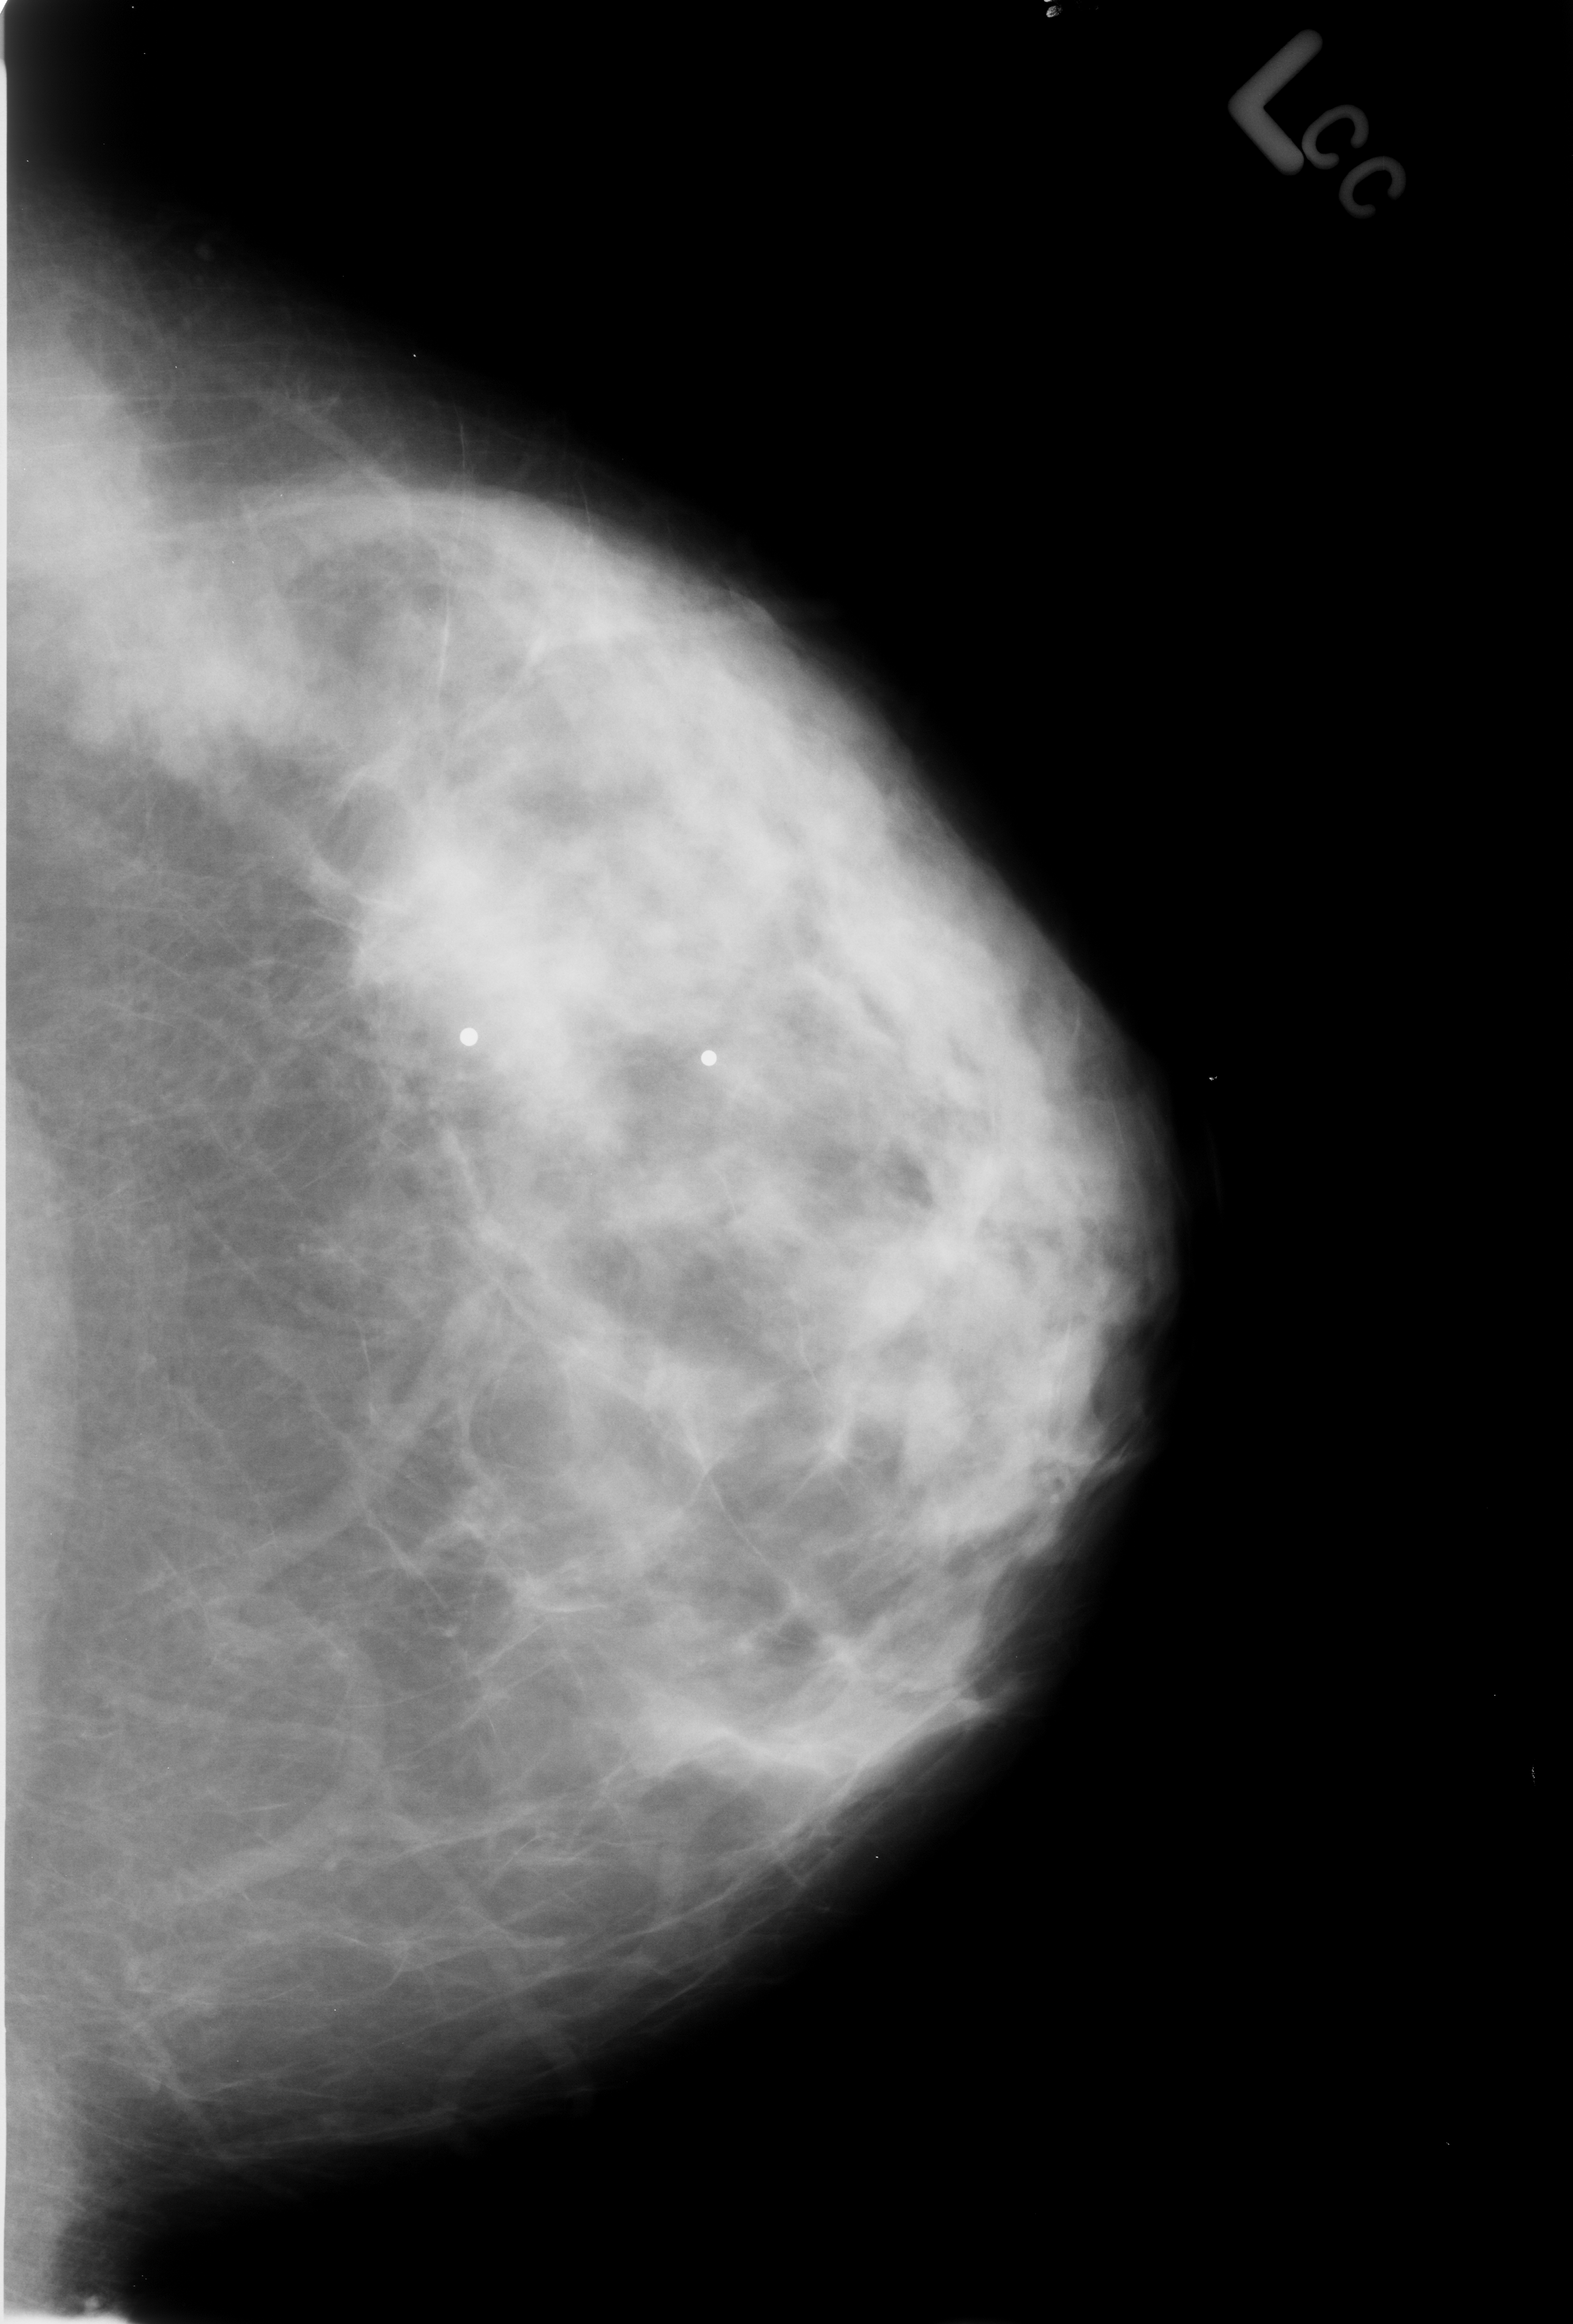
Mammogram (digitized film), left breast, CC view, BI-RADS breast density category 3 (scale 1–4).
Abnormality record for this image: mass, shape focal asymmetric density; BI-RADS assessment category 2; subtlety rating 4 on a 1 (subtle) to 5 (obvious) scale; benign; no additional work-up was recommended (benign without callback).